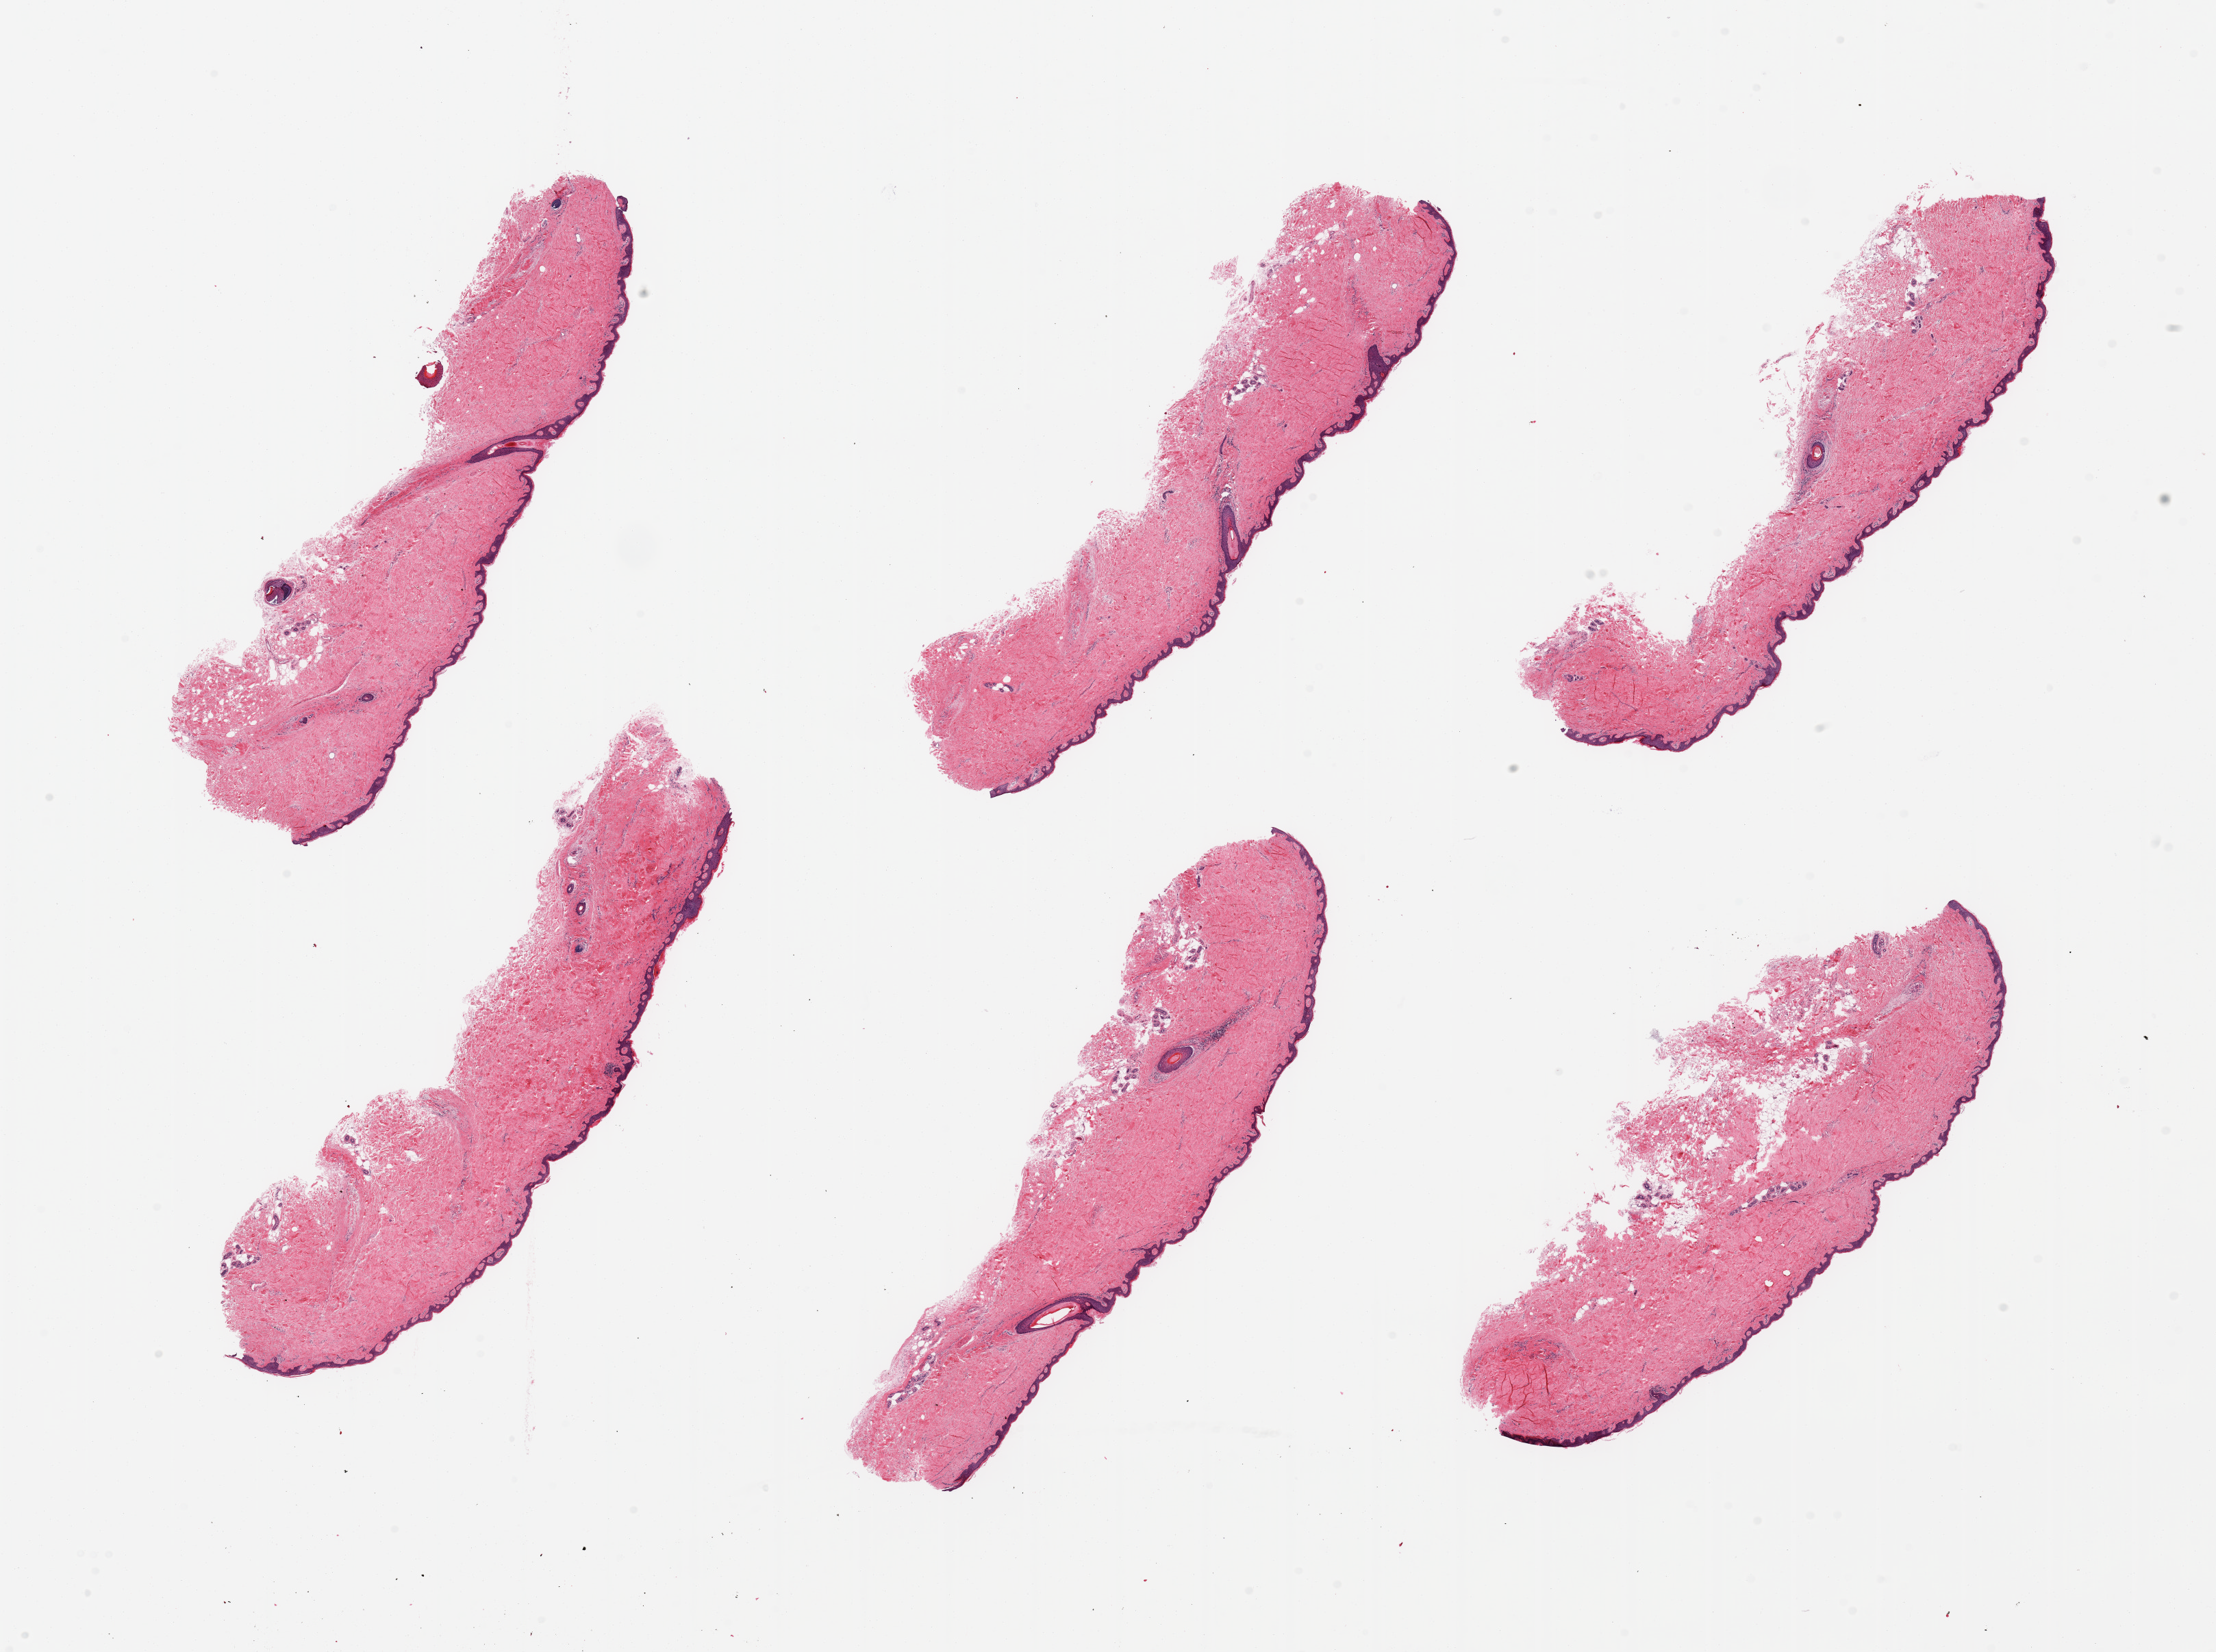
Whole-slide image, haematoxylin and eosin stain, whole scanned area (about 25.6 x 19.1 mm, slide scanned at 20x) shown as a low-resolution overview. PAXgene-fixed paraffin-embedded (PFPE) section. Sampled site (target tissue): skin of suprapubic region. Donor tissue sample.
Reviewer comment on this tissue sample: 6 pieces, no significant dermal fat; squamous epithelium is ~40 microns.